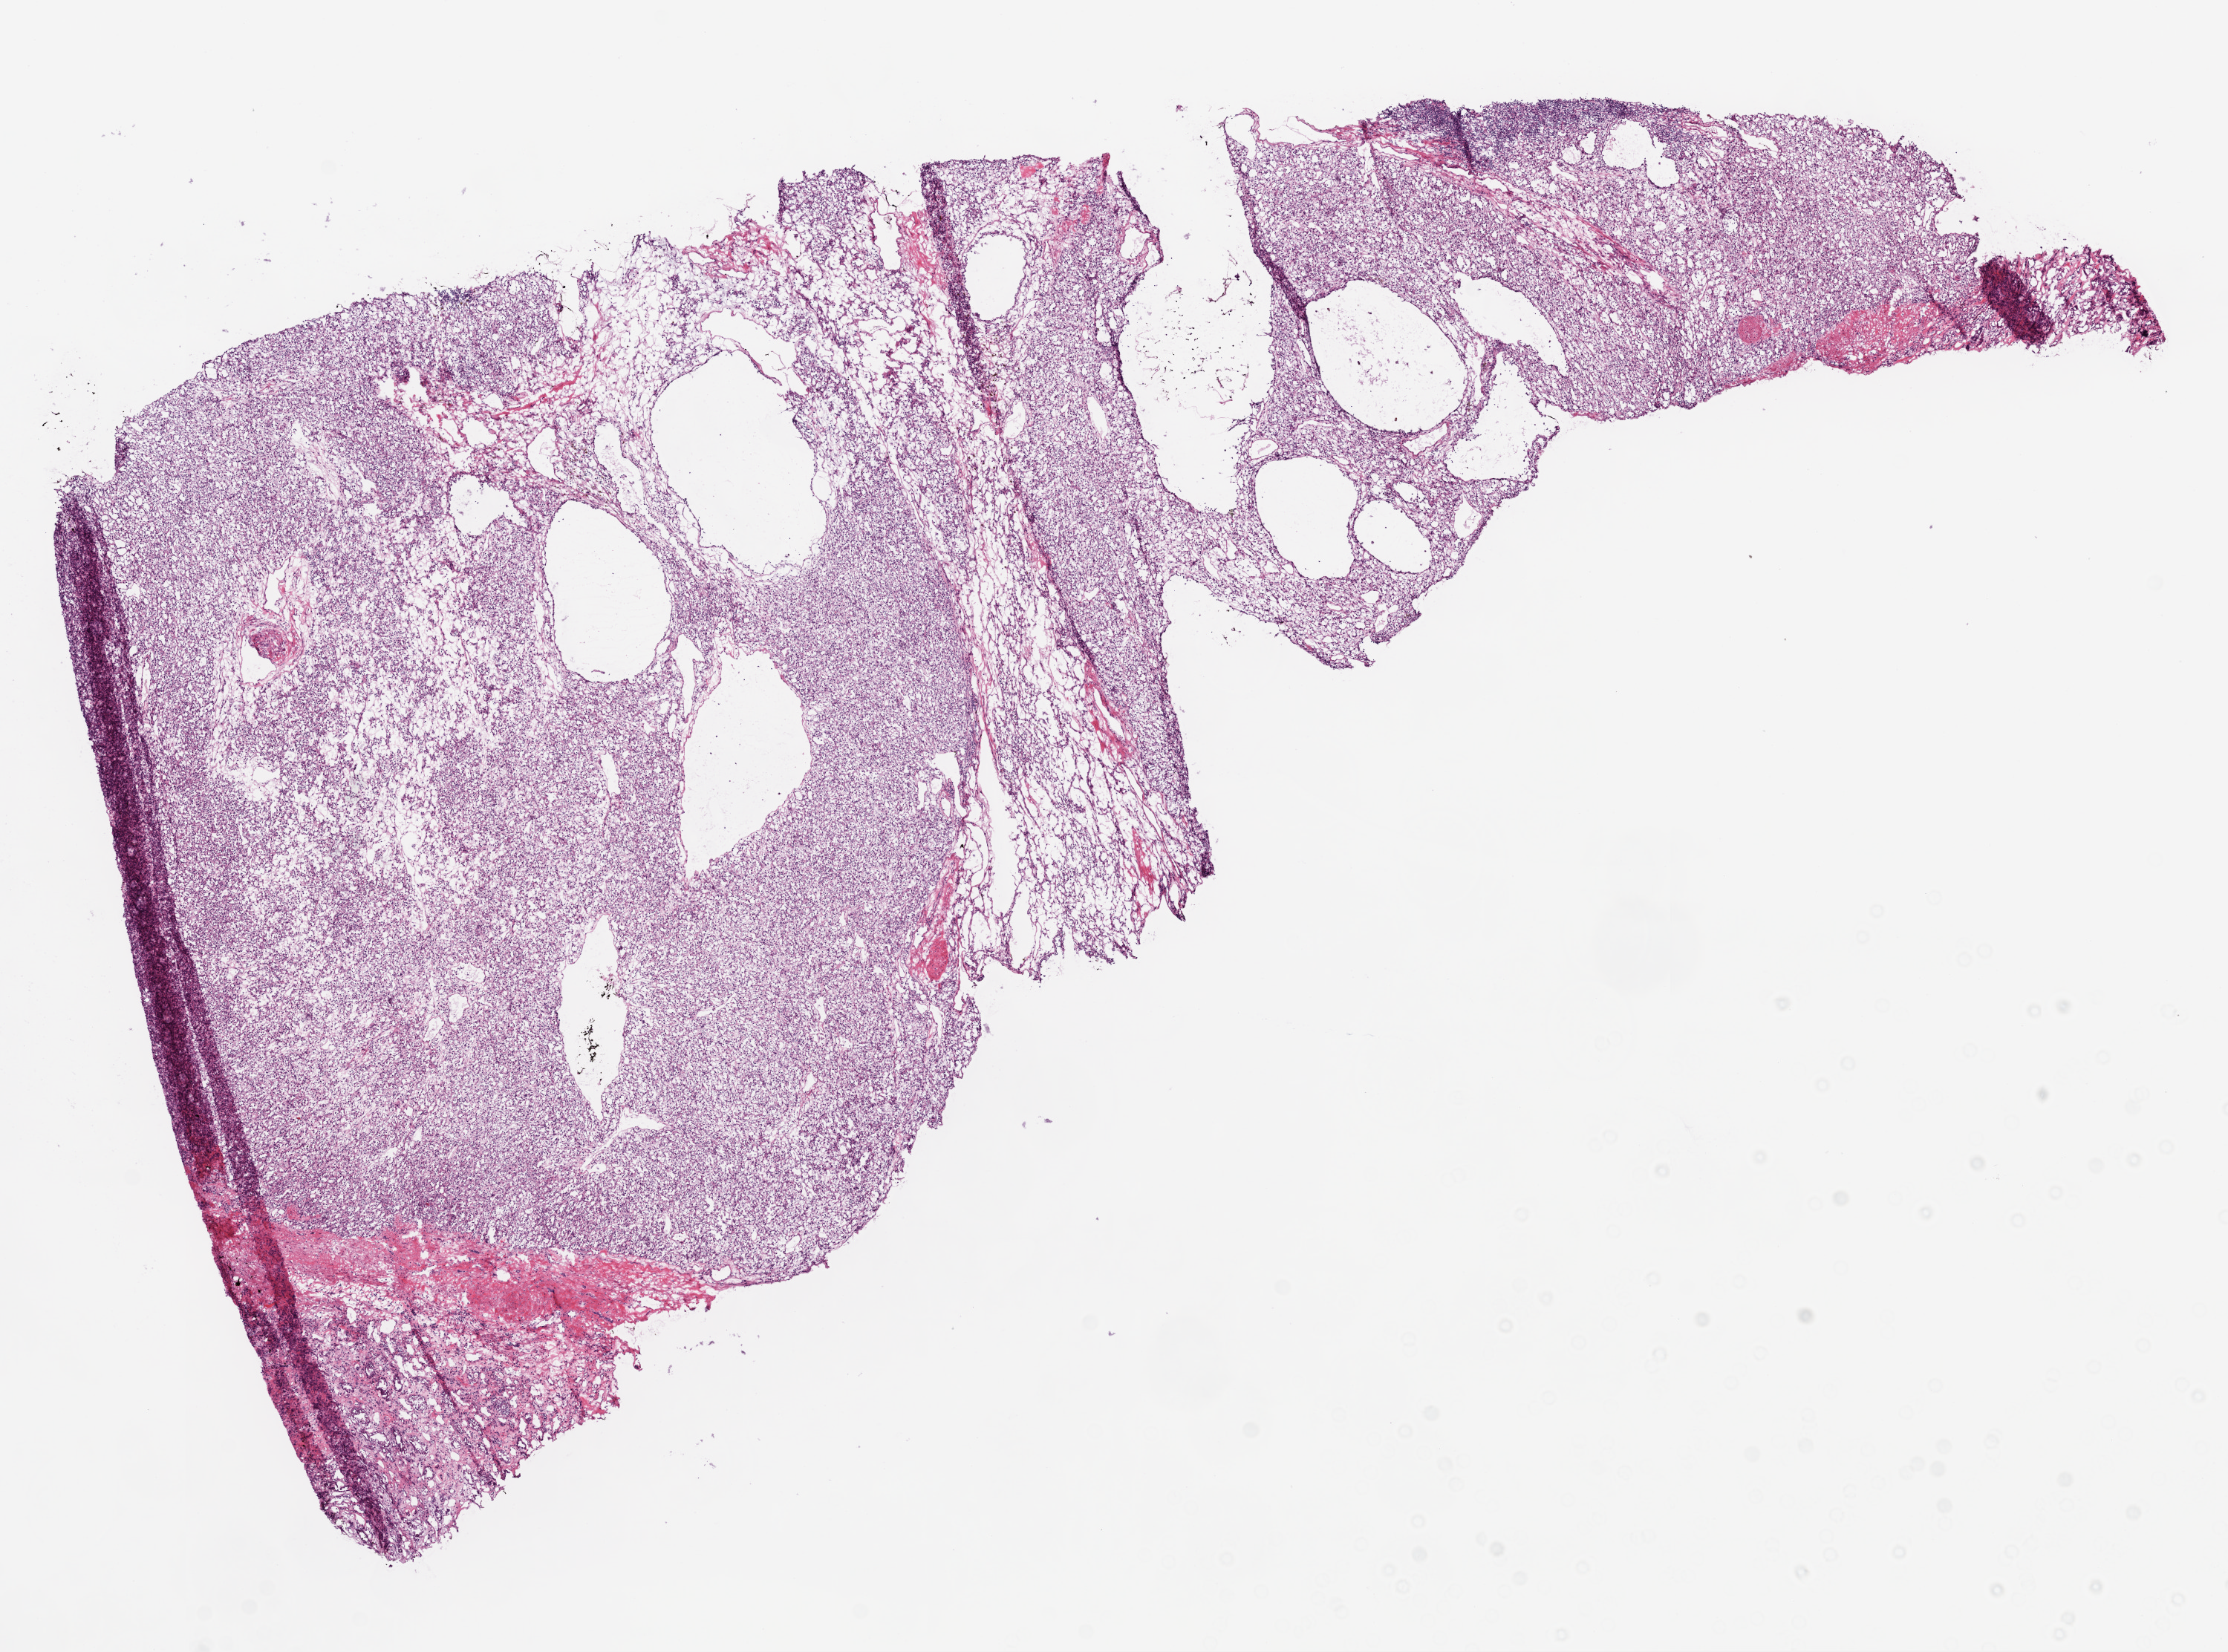
Whole-slide histology image, H&E, a low-resolution overview of the entire scanned area, about 12.0 x 8.9 mm, frozen section from the top of the tissue portion, primary tumour sample from the kidney. Patient: male, age at initial diagnosis 46 years. Histologic grade: G2 (moderately differentiated). Pathologist review of this section (percent, as recorded): tumour cells 90%, tumour nuclei 85%, normal cells 5%, stromal cells 5%, necrosis 0%.
* pathologic diagnosis: Clear cell adenocarcinoma, NOS
* AJCC pathologic stage: I